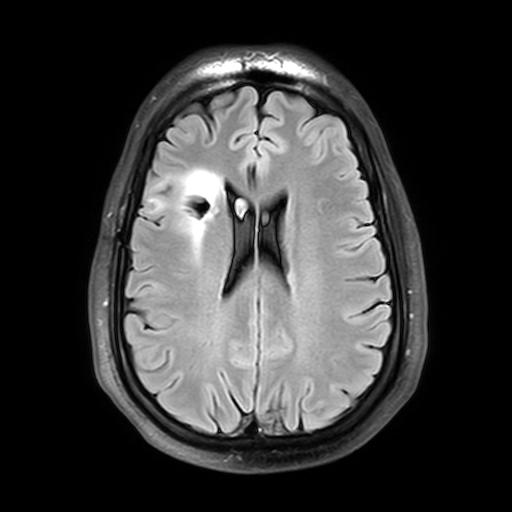
Brain MRI from a brain-tumour surgery series, one axial slice. Position 16 of 42 along the scan axis. T2 FLAIR. 512 × 512 image matrix, field of view 240 × 240 mm. From the clinical record (not read from this slice): histopathology: Astrocytoma; WHO grade: 2; IDH mutation: yes; tumour location: Right Insular.
Structures marked on this image (outlined manually by an expert reader):
- tumour: bounding box <137,169,223,252> (left, top, right, bottom; pixels)